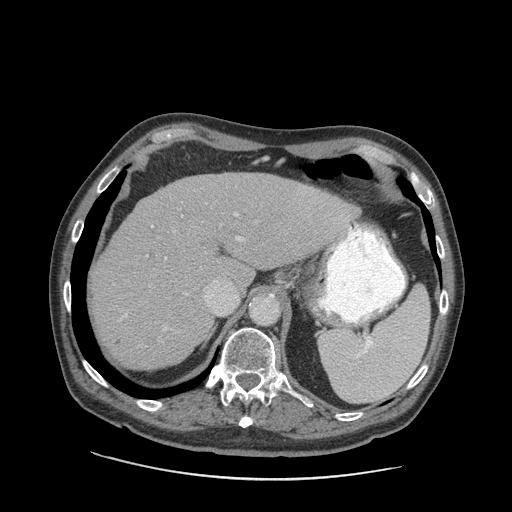
Contrast-enhanced abdominal CT (liver protocol), one axial slice; slice 64 of 89 in the series (ordered by position); 140 kVp; soft-tissue window (W 400 / L 40 HU); 2.5 mm slice thickness; 512 × 512 image matrix, field of view 420 × 420 mm. Case-level facts recorded for this patient, not image findings: diagnosis: hepatocellular carcinoma (patient treated with transarterial chemoembolisation; whether this scan precedes or follows treatment is not stated here); TNM stage (as recorded): Stage-I; Child-Pugh class: A; tumour nodularity: uninodular; tumour size: 4.6 cm.
Annotated regions visible in this slice (semi-automatically segmented with operator editing):
- liver parenchyma outside the tumour (the mass and vessels are separate outlines, so this box may not span the whole liver): bounding box (x1, y1, x2, y2) in pixels: (94, 172, 358, 370)
- liver vessels: (118, 186, 349, 332)